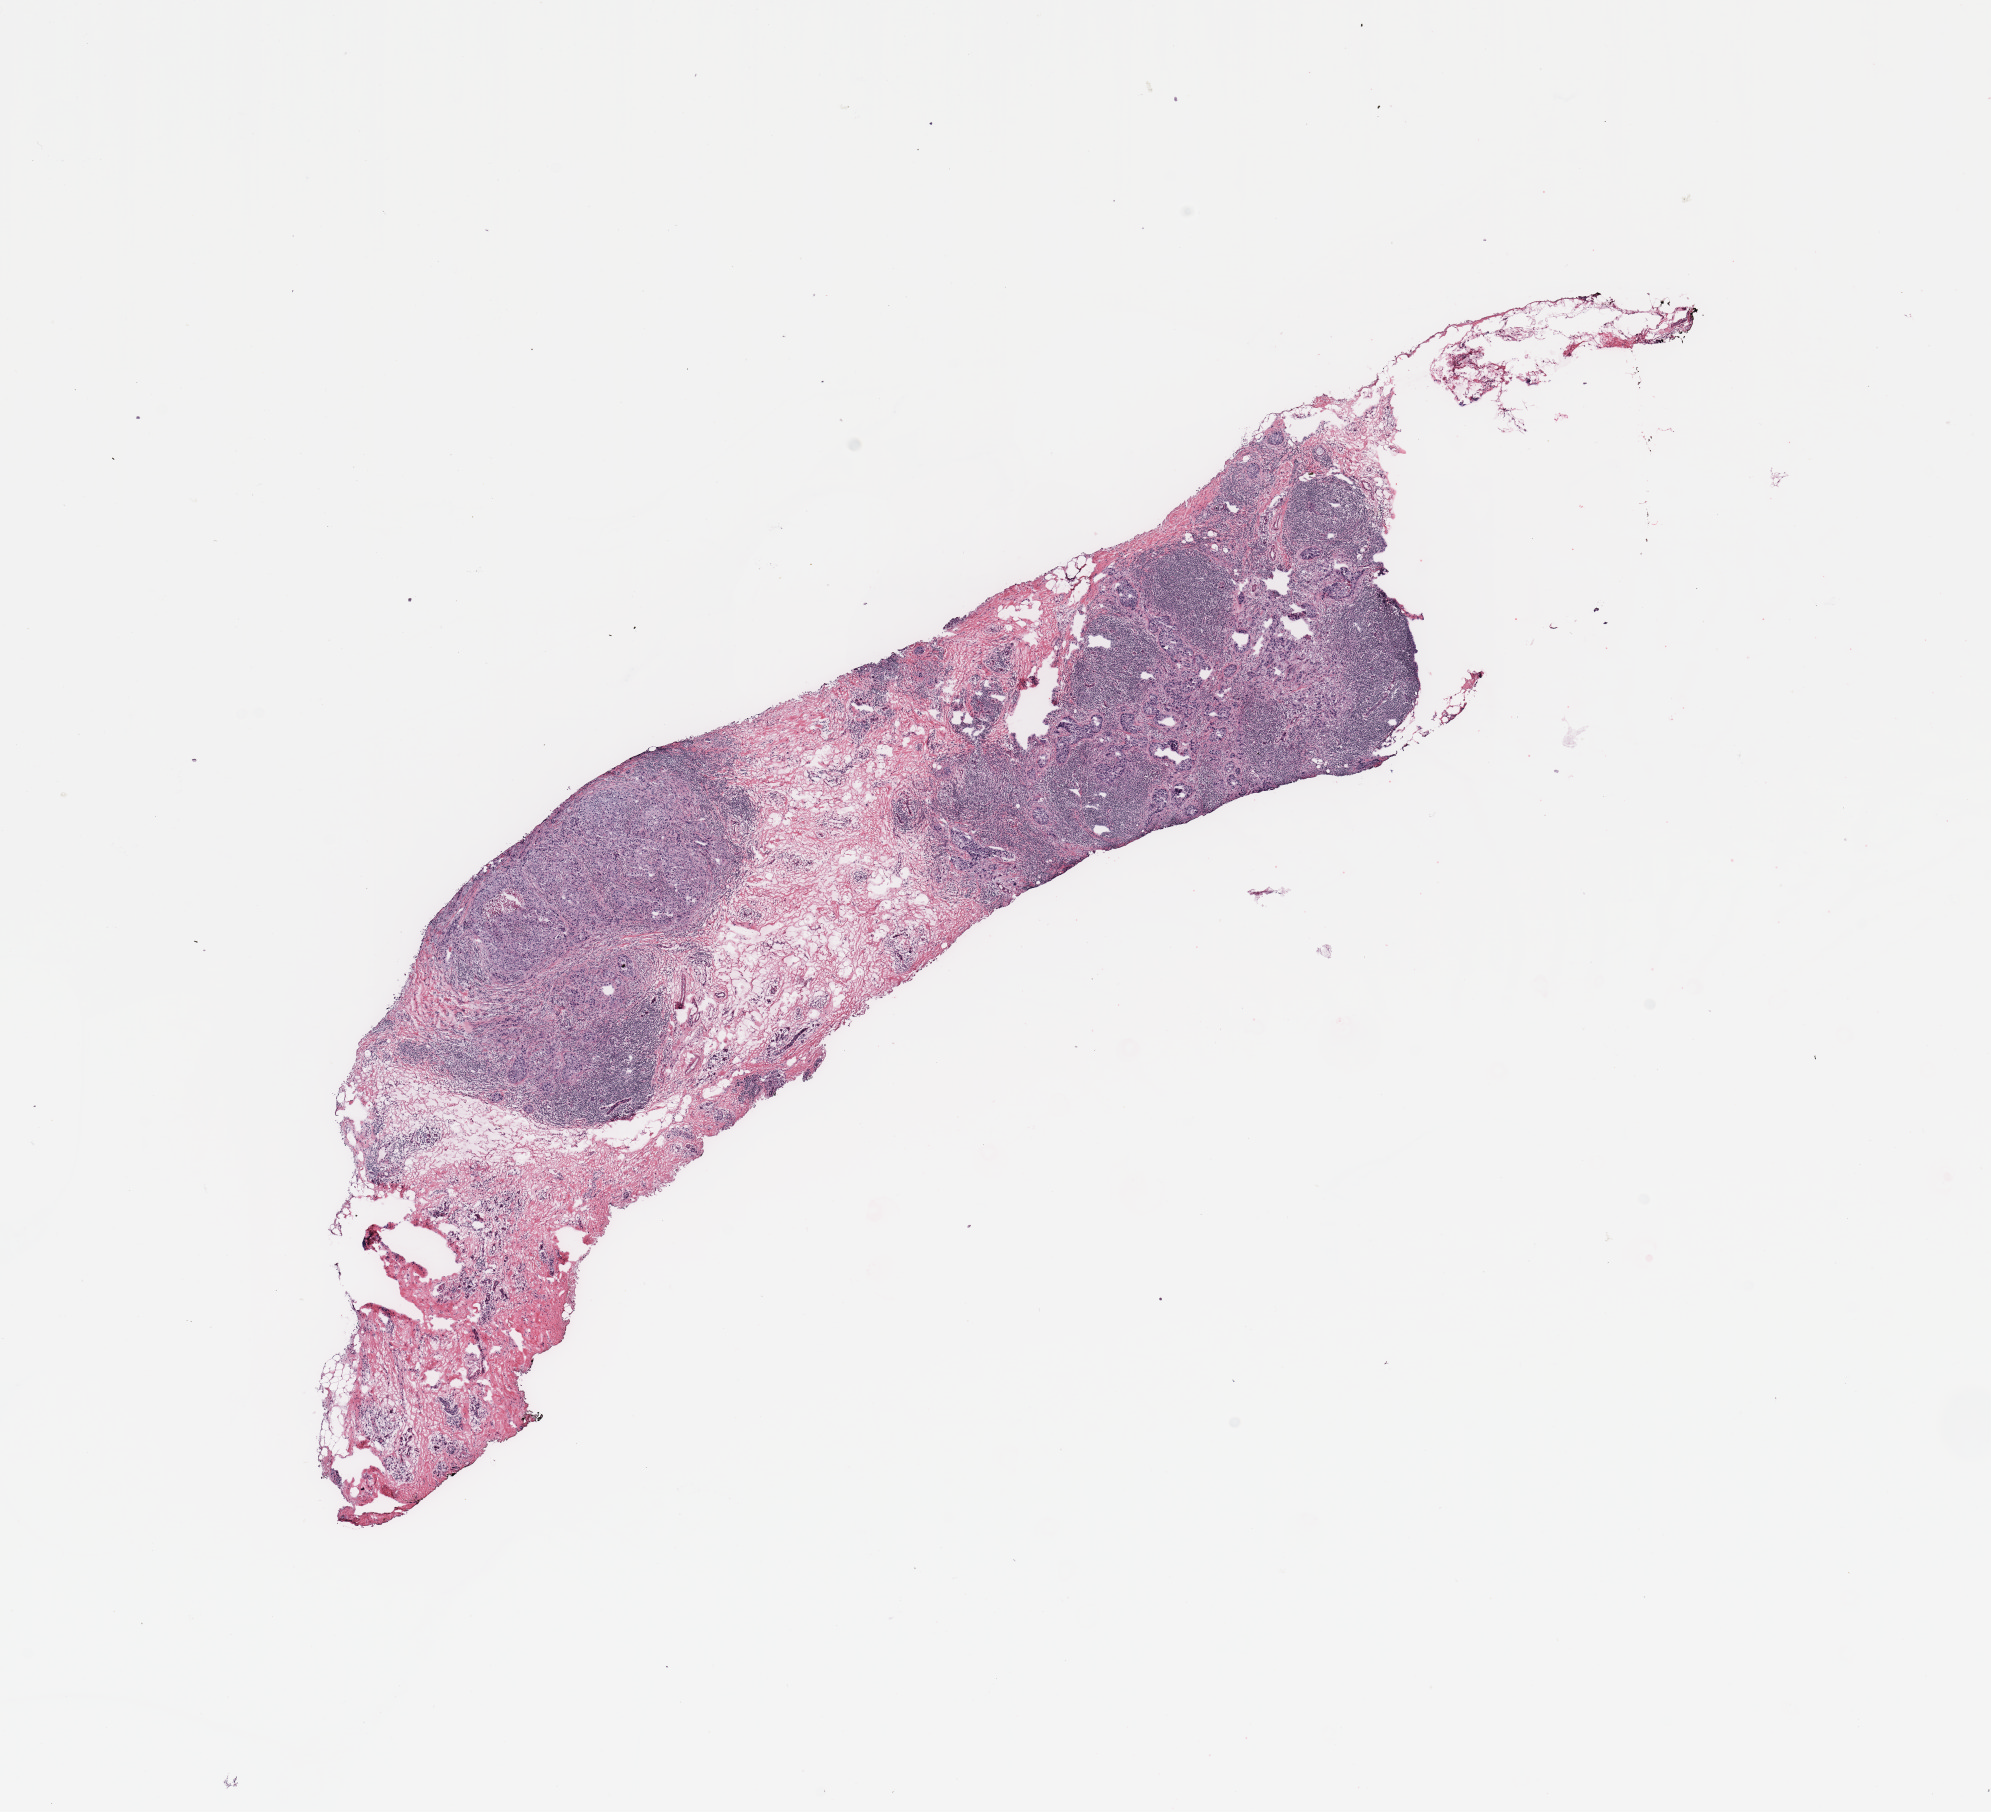
H&E whole-slide image — low-resolution overview of the scanned area, about 15.8 x 14.3 mm. Breast, tissue type not recorded.
- patient diagnosis (cohort enrolment): breast cancer (breast)